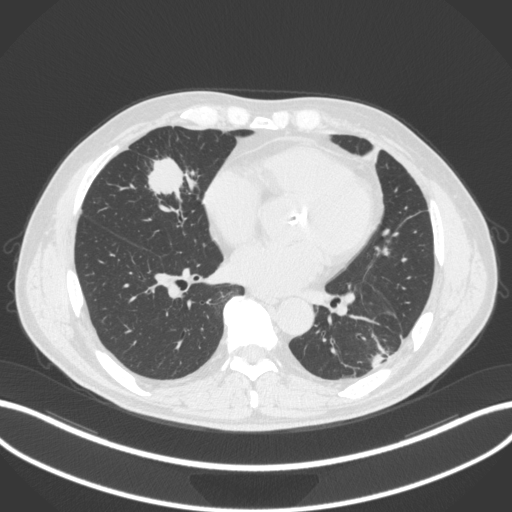
Chest CT, one axial slice; slice 117 of 399 in the series (ordered by position); reconstruction kernel B31f; 120 kVp; lung window (W 1500 / L -600 HU); 1 mm slice thickness; 512 × 512 image matrix, field of view 400 × 400 mm. Patient: male, 59 years. From the clinical record (not read from this slice): clinical TNM (as recorded): T2a N1 M0.
Annotated regions visible in this slice (bounding box drawn by a radiologist):
- lung tumour (recorded histology: adenocarcinoma): bounding box (x1, y1, x2, y2) in pixels: (140, 150, 198, 207)